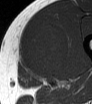
MRI of an extremity soft-tissue mass, one axial slice; position 31 of 62 along the scan axis; MR volume resampled by the dataset authors to the PET/CT grid (not the native acquisition matrix); 92 × 104 image matrix, field of view 90 × 102 mm. Male patient. From the clinical record (not read from this slice): histological type: mixoid liposarcoma; grade: low; site of the primary tumour: left thigh.
Annotated regions visible in this slice (expert contour drawn on MRI and transferred to this co-registered scan by the dataset authors):
- gross tumour volume (mass): bounding box <21,22,70,80> (left, top, right, bottom; pixels)